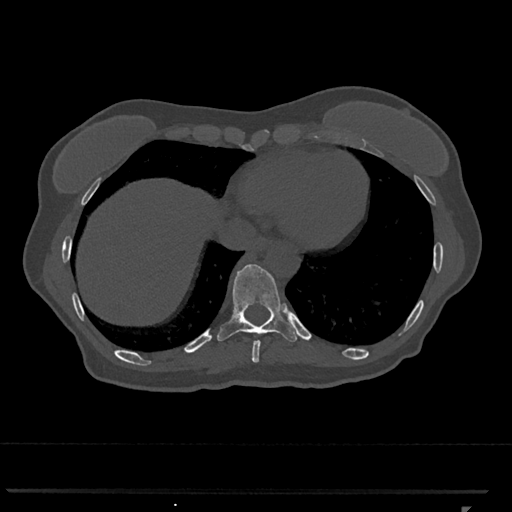
CT including the spine, one axial slice. 120 kVp. Bone window (W 1800 / L 400 HU). 512 × 512 image matrix. Patient: female, 62 years. Case-level facts recorded for this patient, not image findings: primary cancer: renal.
Structures marked on this image (semi-automatically segmented with operator editing):
- T10 vertebra: bounding box (x1, y1, x2, y2) in pixels: (217, 264, 299, 344)
- T9 vertebra: (251, 341, 260, 363)